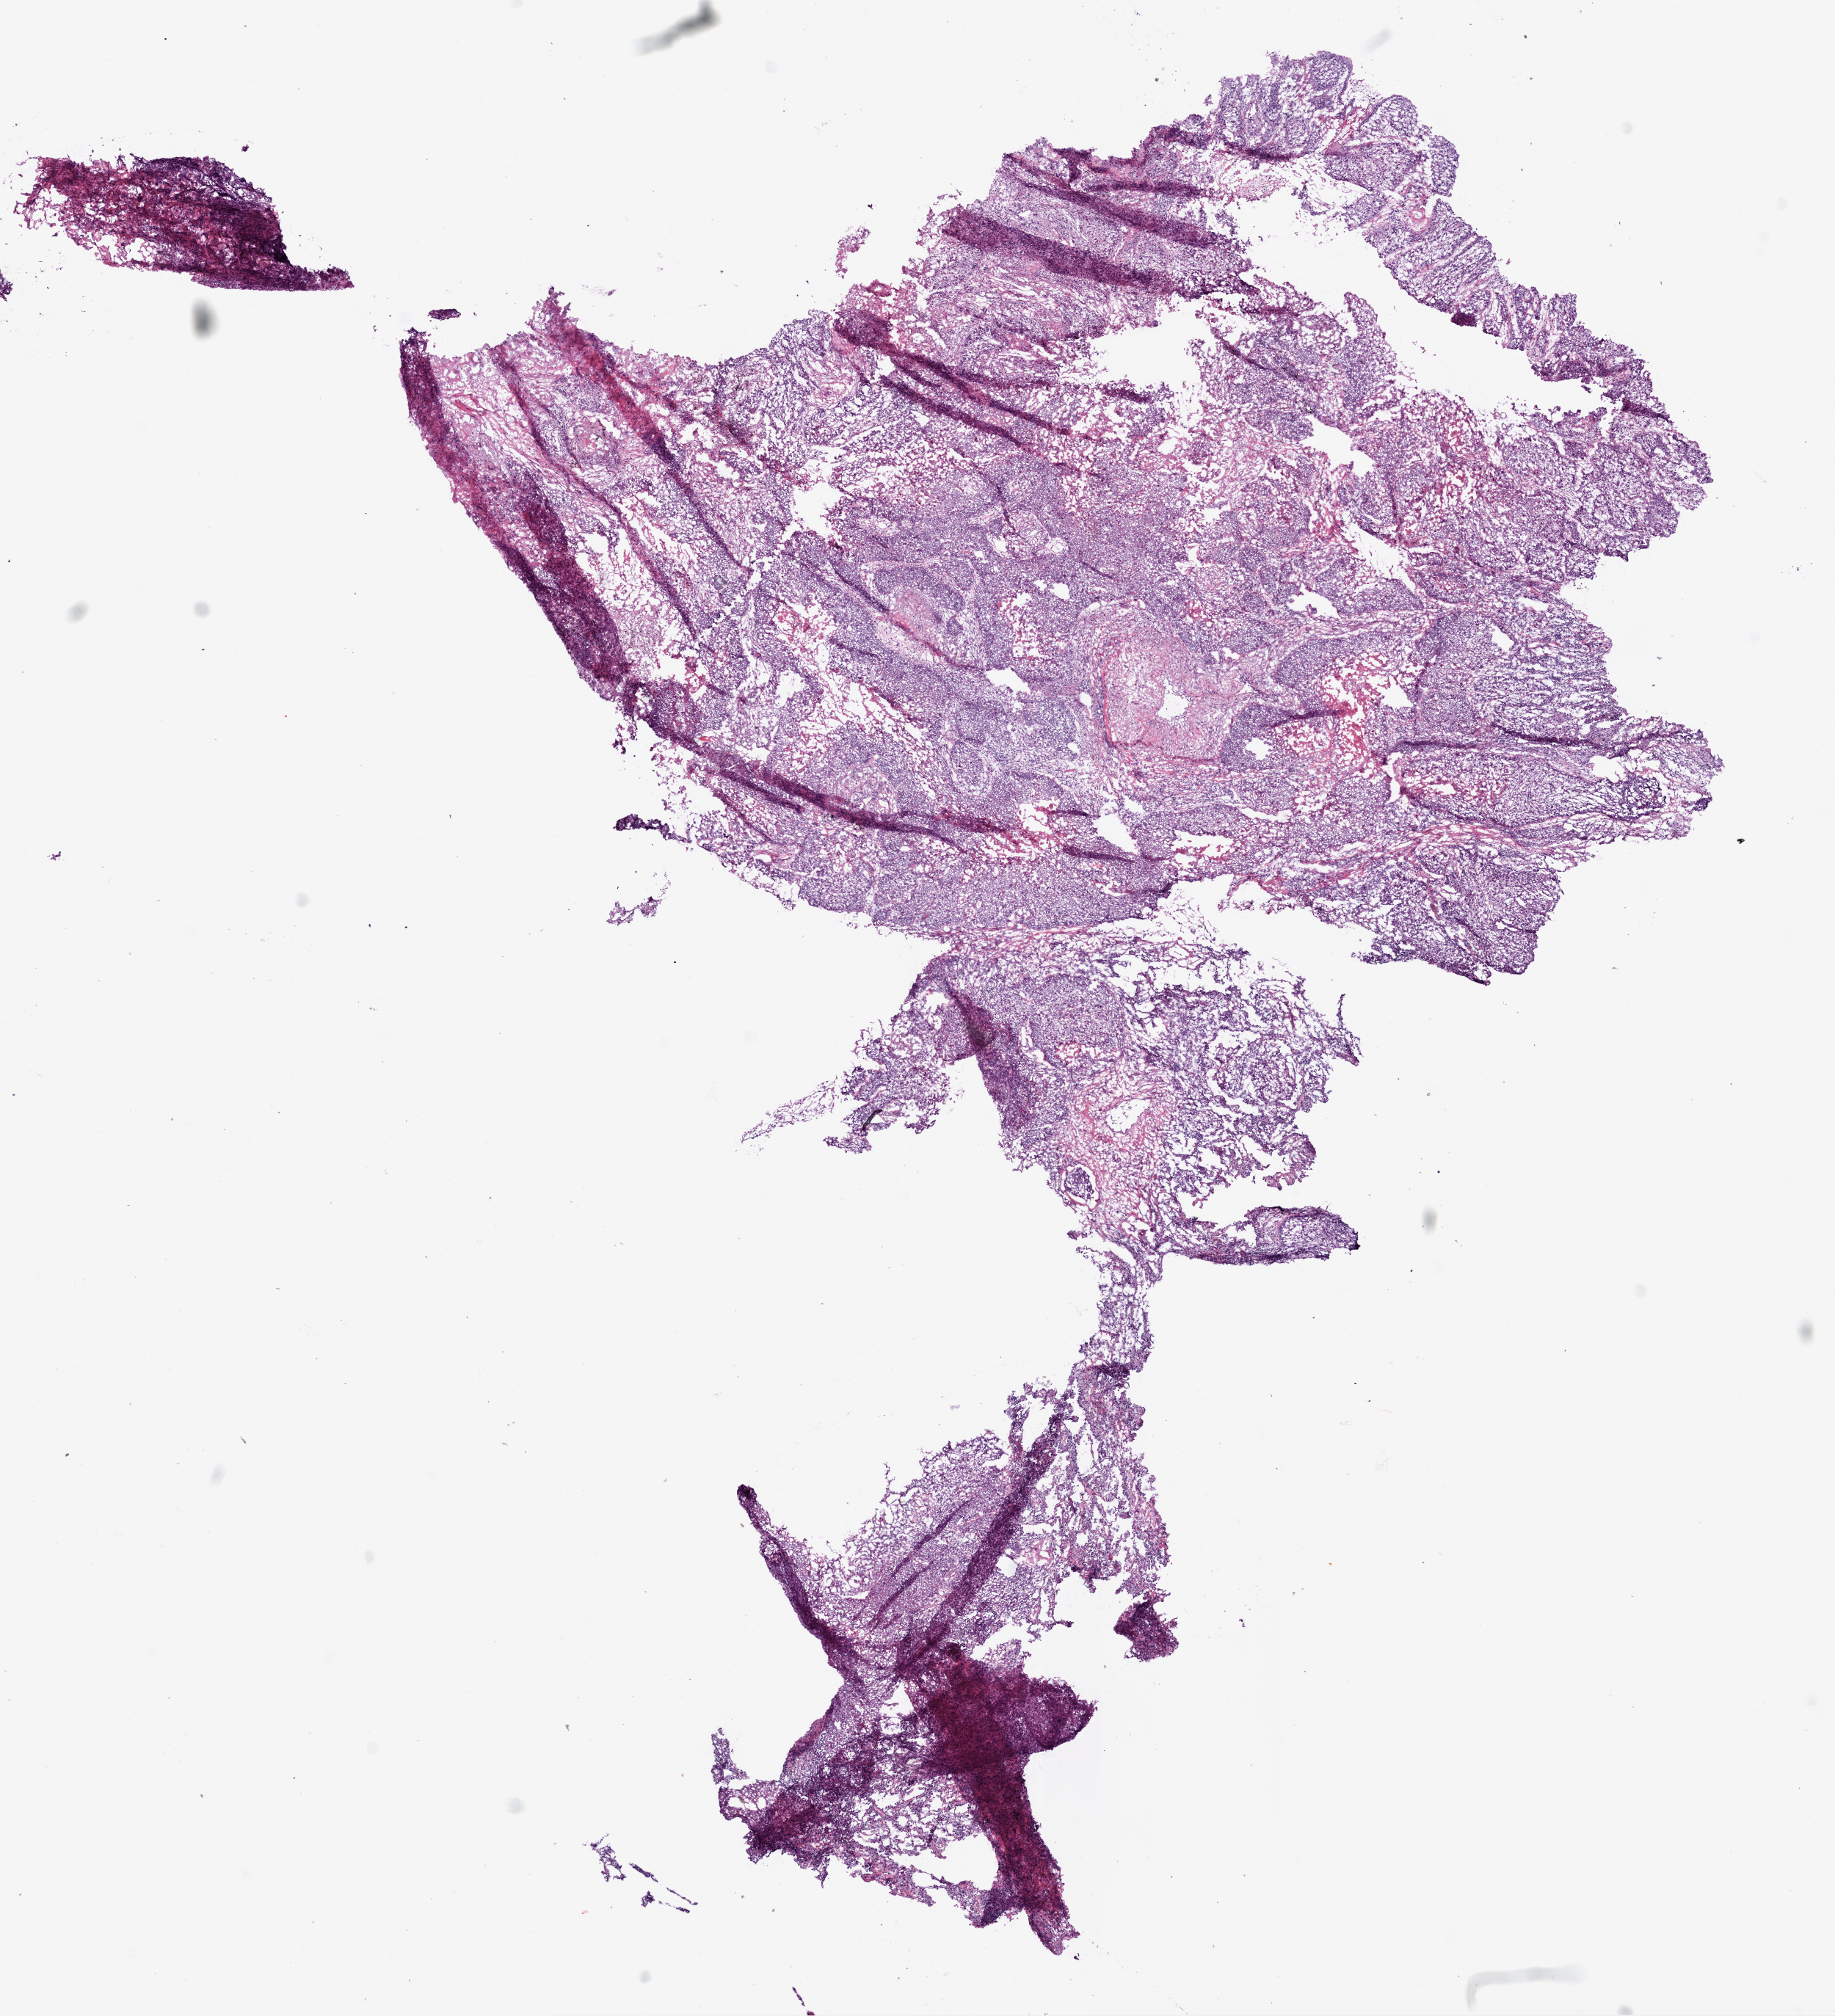
Whole-slide histology image, Hematoxylin and eosin (H&E) stained — whole scanned area (about 10.0 x 11.0 mm) shown as a low-resolution overview, frozen section, primary tumour sample from the lung. Male patient; age at initial diagnosis 73 years. Composition of this section per pathologist review: tumour cells 81%, tumour nuclei 75%, normal cells 2%, stromal cells 7%, necrosis 10%.
Laterality: left. Diagnosis: Squamous cell carcinoma, NOS (lower lobe, lung). AJCC pathologic stage: IIIB.